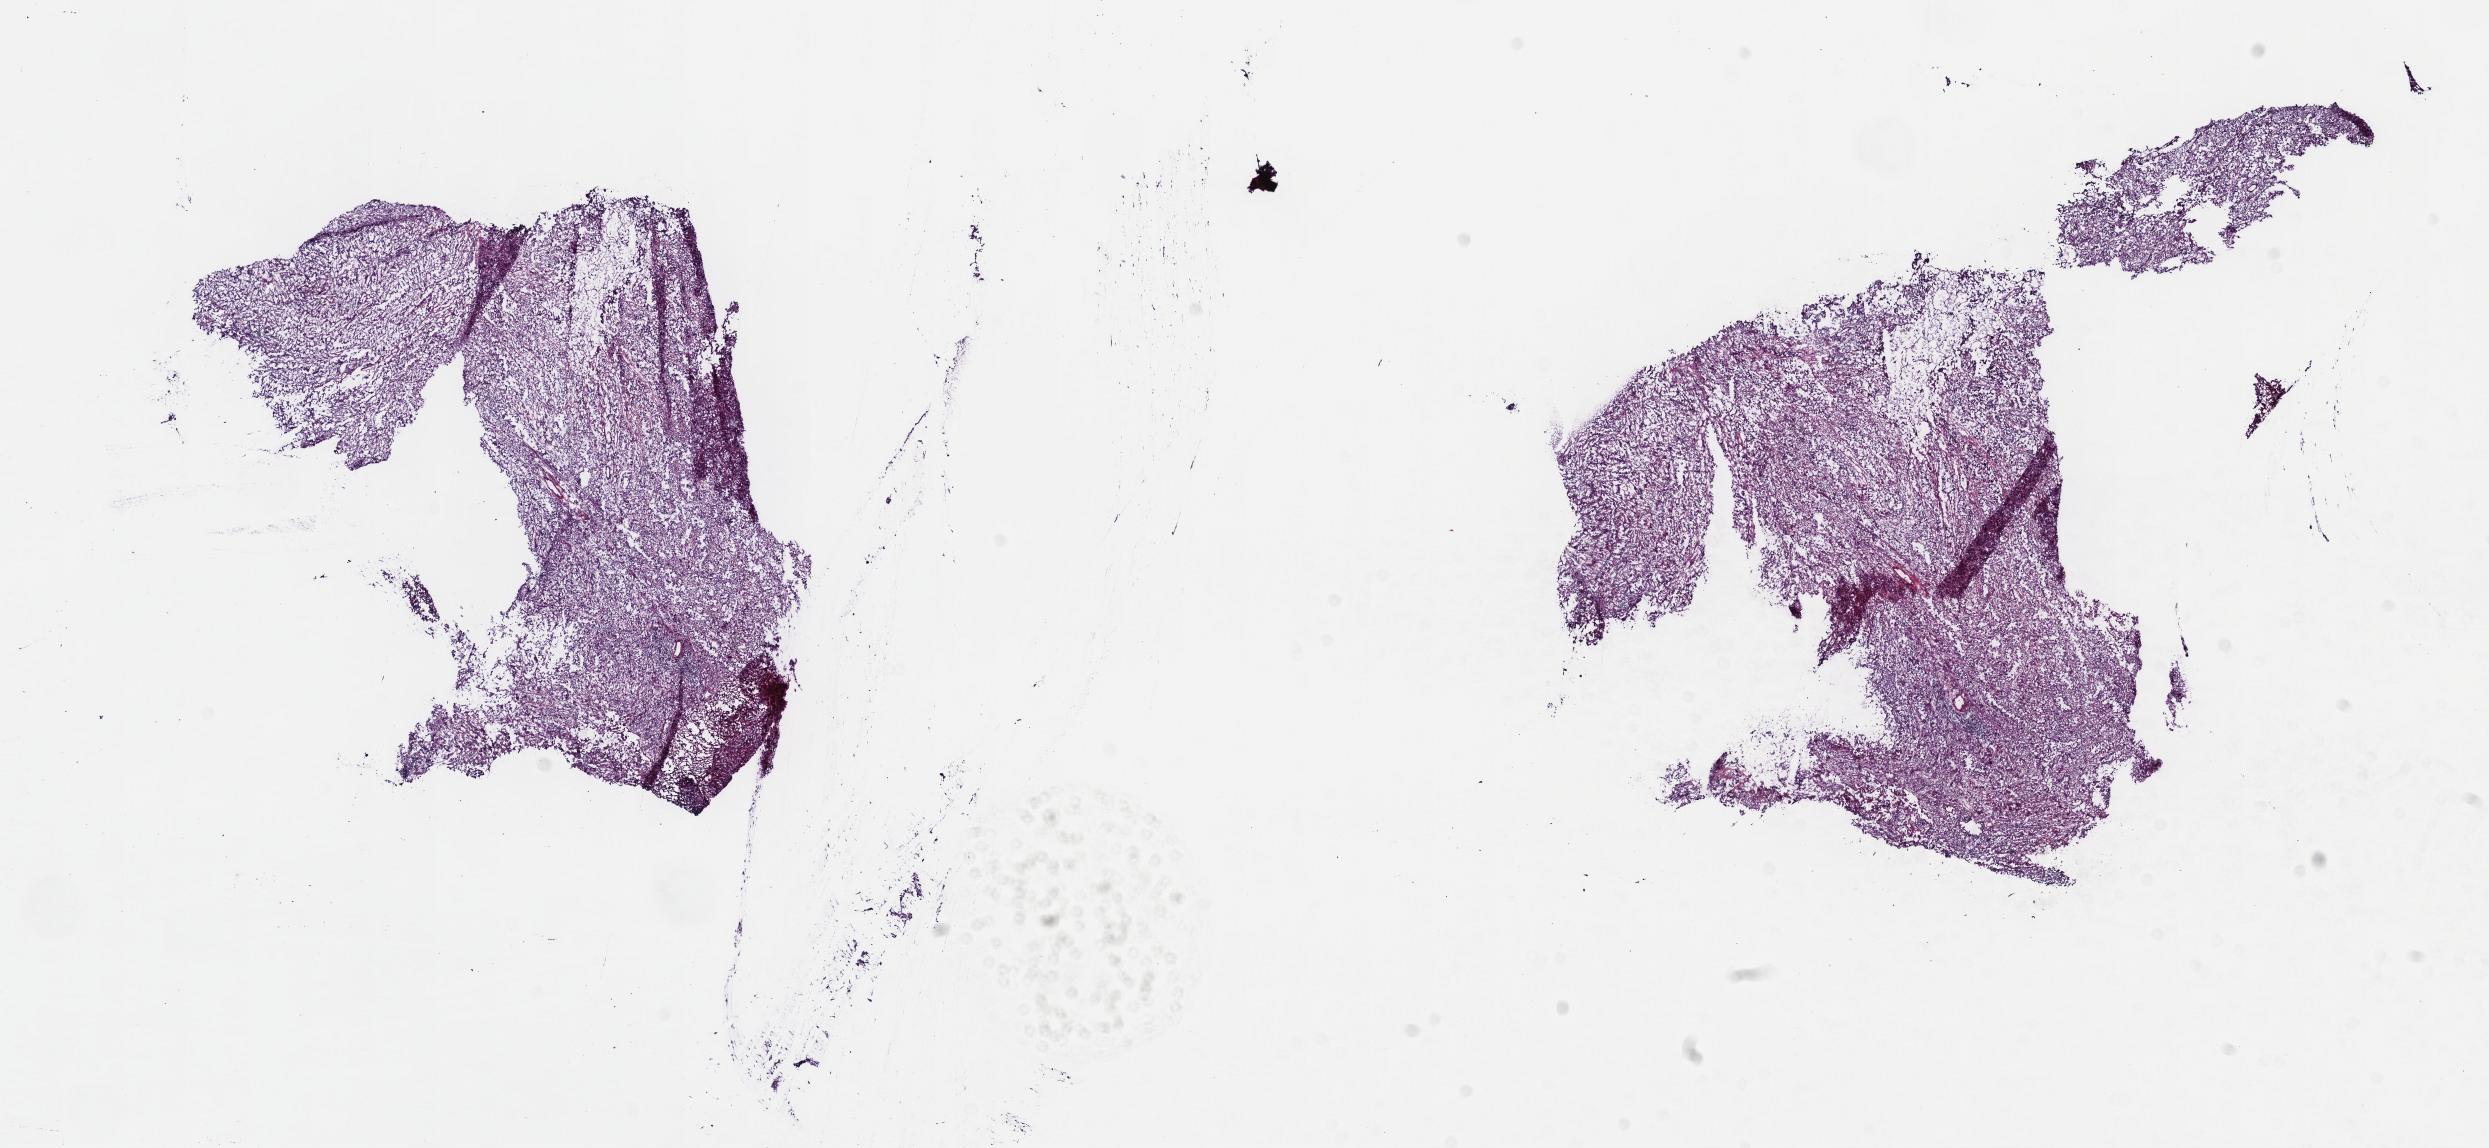
Whole-slide histology image, H&E — shown as a low-resolution overview of the whole scanned area (about 20.1 x 9.3 mm, from a 40x scan), frozen section from the top of the tissue portion, sample: primary tumour, bladder. Female, age 69 years at initial diagnosis. Histologic grade: high grade. Slide review estimates, as recorded: tumour cells 60%, tumour nuclei 70%, normal cells 0%, stromal cells 30%, necrosis 10%. Inflammatory infiltration, as recorded: lymphocyte infiltration 90%, monocyte infiltration 10%, neutrophil infiltration 0%.
AJCC pathologic stage: II. Diagnosis: Transitional cell carcinoma.